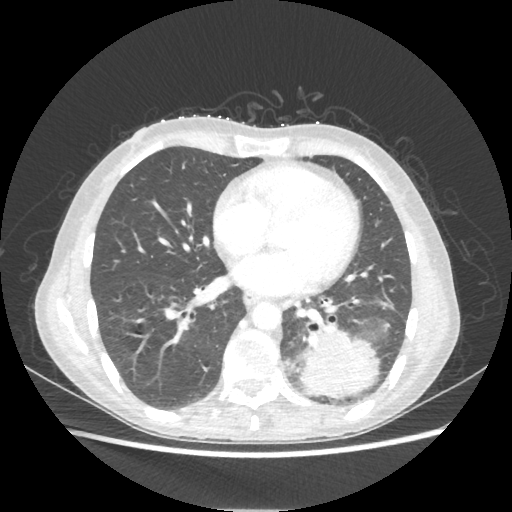
Chest CT, one axial slice; slice 92 of 221 in the series (ordered by position); reconstruction kernel STANDARD; 80 kVp; lung window (W 1500 / L -600 HU); 1.25 mm slice thickness; 512 × 512 image matrix, field of view 360 × 360 mm. Female patient, age 53 years. From the clinical record (not read from this slice): clinical TNM (as recorded): T3 N0 M0.
Structures marked on this image (bounding box drawn by a radiologist):
- lung tumour (recorded histology: adenocarcinoma): bounding box [x1, y1, x2, y2] px = [298, 325, 380, 398]